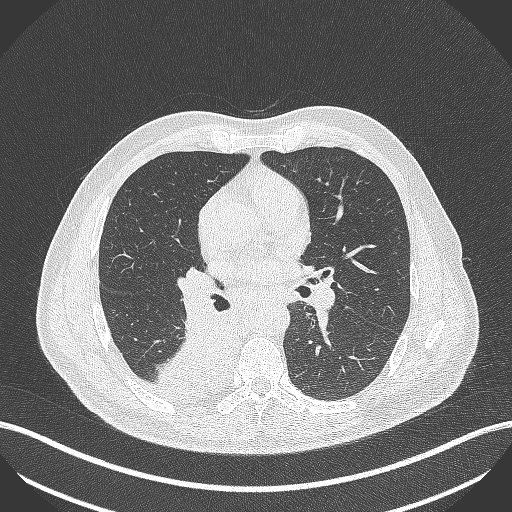
Chest CT, one axial slice. Position 256 of 451 along the scan axis. 100 kVp. Lung window (W 1500 / L -600 HU). 1 mm slice thickness. 512 × 512 image matrix, field of view 400 × 400 mm. Male patient, age 61 years. From the clinical record (not read from this slice): clinical TNM (as recorded): T1 N0 M0; histopathological grade: G3.
Annotated regions visible in this slice (bounding box drawn by a radiologist):
- lung tumour (recorded histology: small cell carcinoma): bounding box (x1, y1, x2, y2) in pixels: (155, 307, 240, 405)